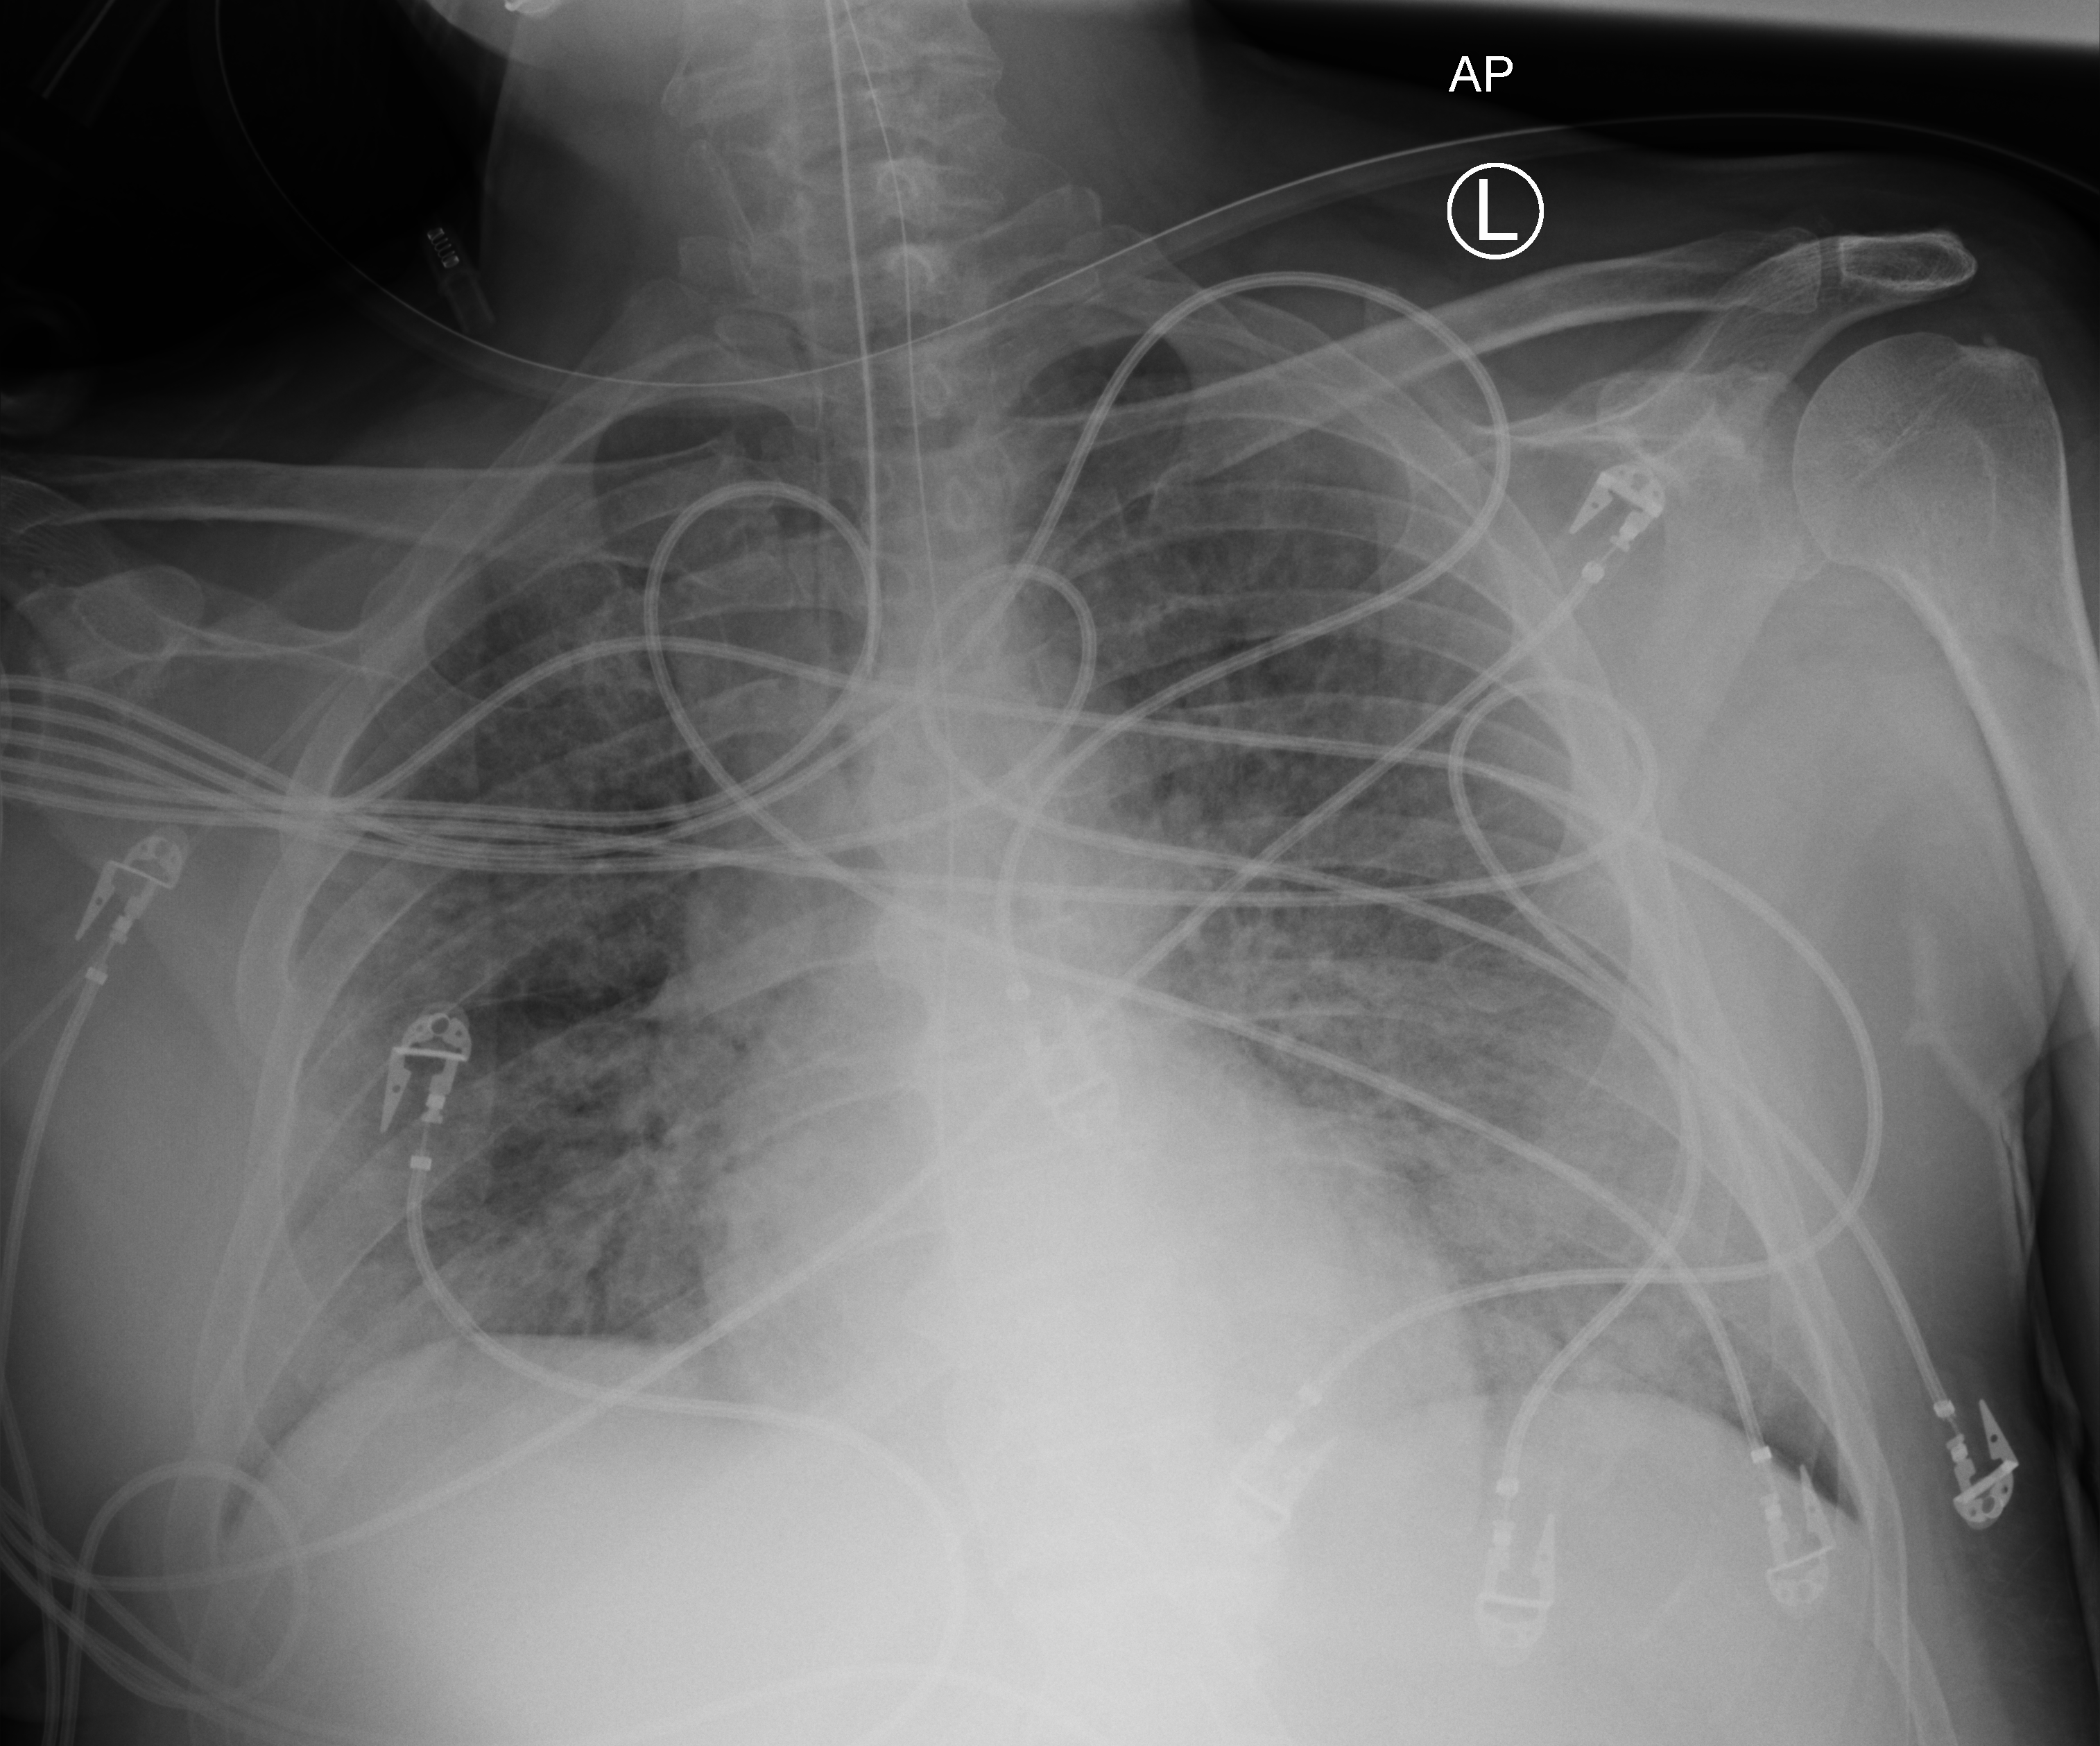
Bedside chest radiograph (computed radiography); anteroposterior (AP) projection. Male patient hospitalised with COVID-19, age 60–74 years.
Hospital-stay facts (about this admission, not read from this image; timing relative to this image not recorded): other chronic lung disease (admission record): no.